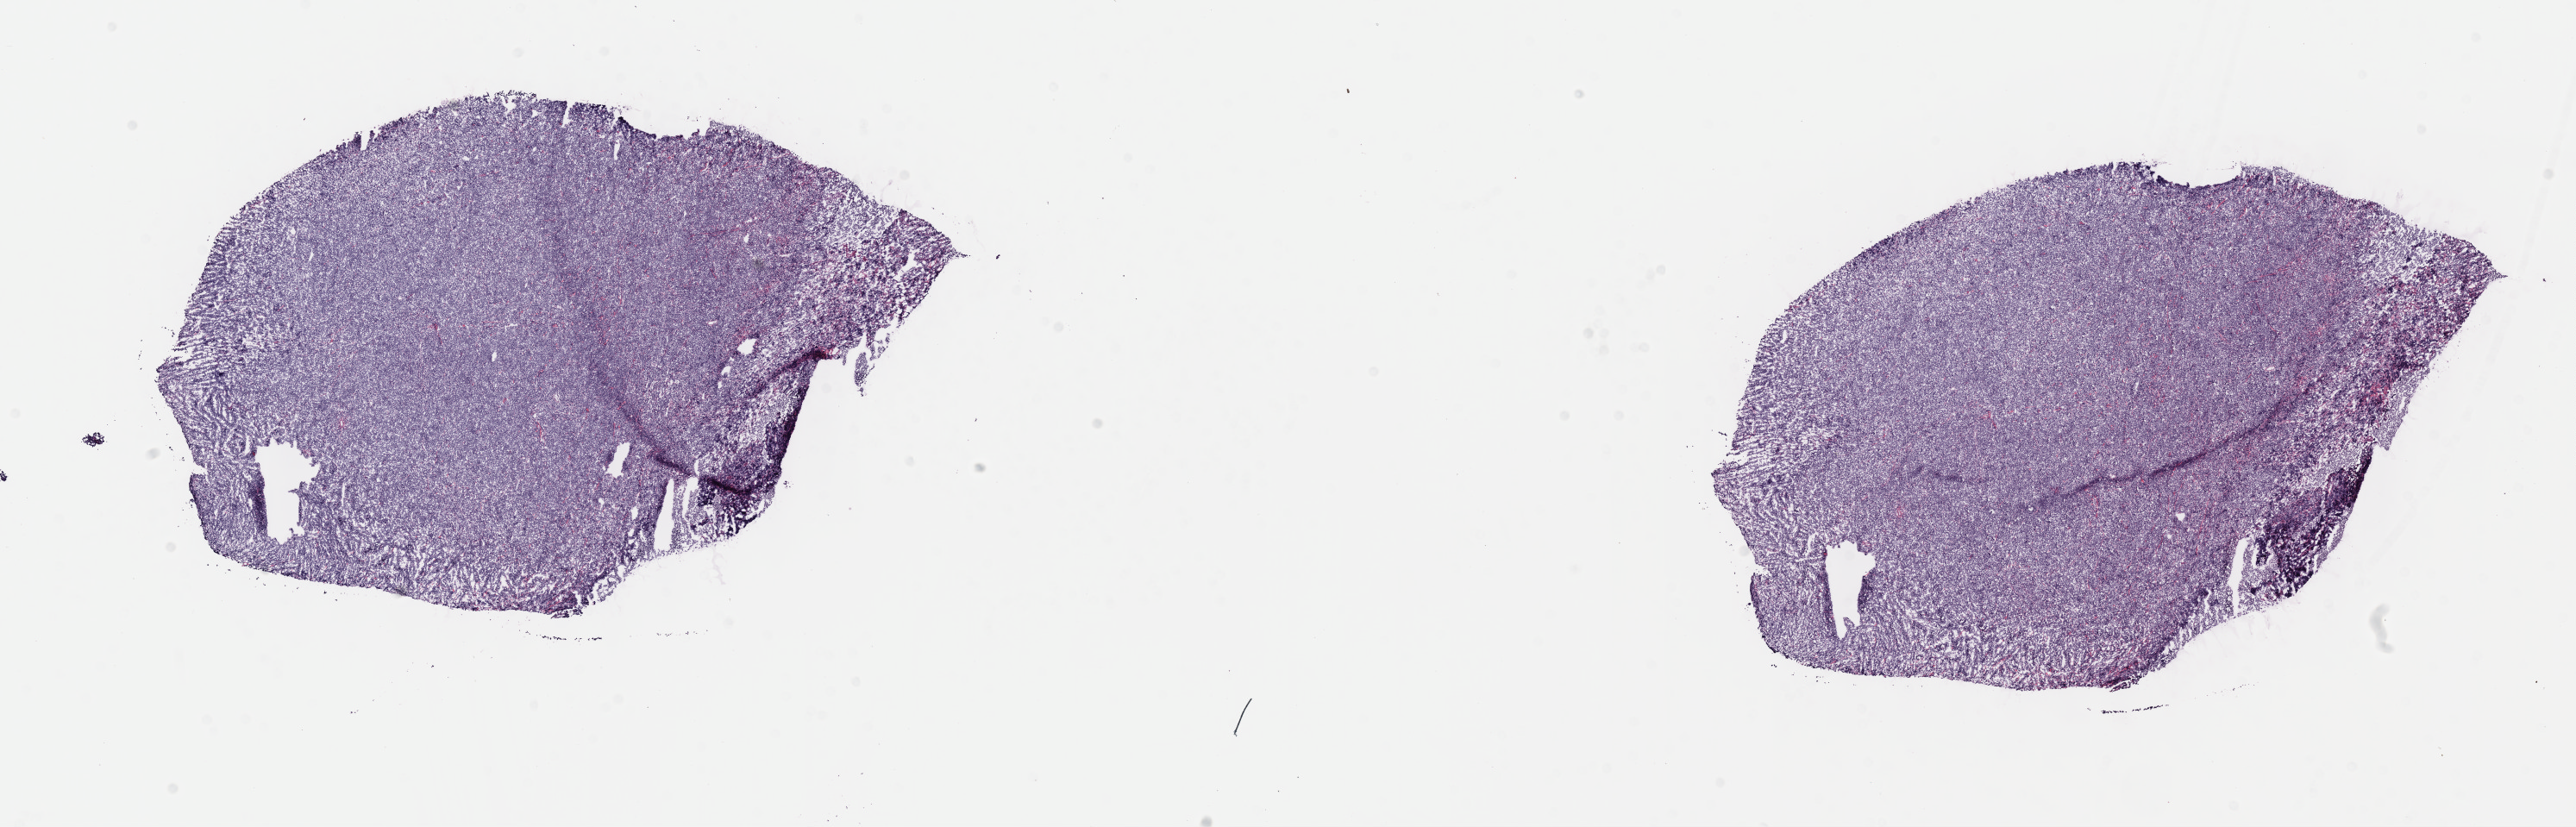
Whole-slide image, hematoxylin and eosin (H&E) stain — shown as a low-resolution overview of the whole scanned area (about 24.2 x 7.8 mm). Frozen section. Primary tumor. Site: mandible. Patient male; age 11 years. Pathologist review of this section (percent, as recorded): tumor cells 95%, tumor nuclei 95%, stromal cells 3%, necrosis 2%, normal cells 0%. Inflammatory infiltration, as recorded: lymphocyte infiltration 3%, monocyte infiltration 5%, neutrophil infiltration 0%.
Ann Arbor stage (patient): Stage III. Diagnosis: Burkitt lymphoma, NOS. Section: bottom of the tissue portion.